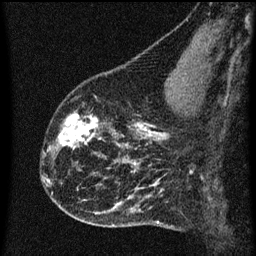
Breast MRI (dynamic contrast-enhanced), one sagittal slice; dynamic contrast-enhanced series, image 2 of 3 at this slice position (ordered by acquisition); 1.5 T; TE 4.2 ms, TR 8 ms; 2 mm slice thickness; 256 × 256 image matrix, field of view 180 × 180 mm. Female patient, age 43 years.
Annotated regions visible in this slice (semi-automatically segmented with operator editing):
- analysis volume of interest (the breast-tissue region the enhancement analysis was run in; not a lesion): bounding box (x1, y1, x2, y2) in pixels: (55, 104, 104, 153)
- tumour enhancement mask (voxels above the 70 % enhancement threshold inside the analysis volume of interest): (58, 114, 102, 149)